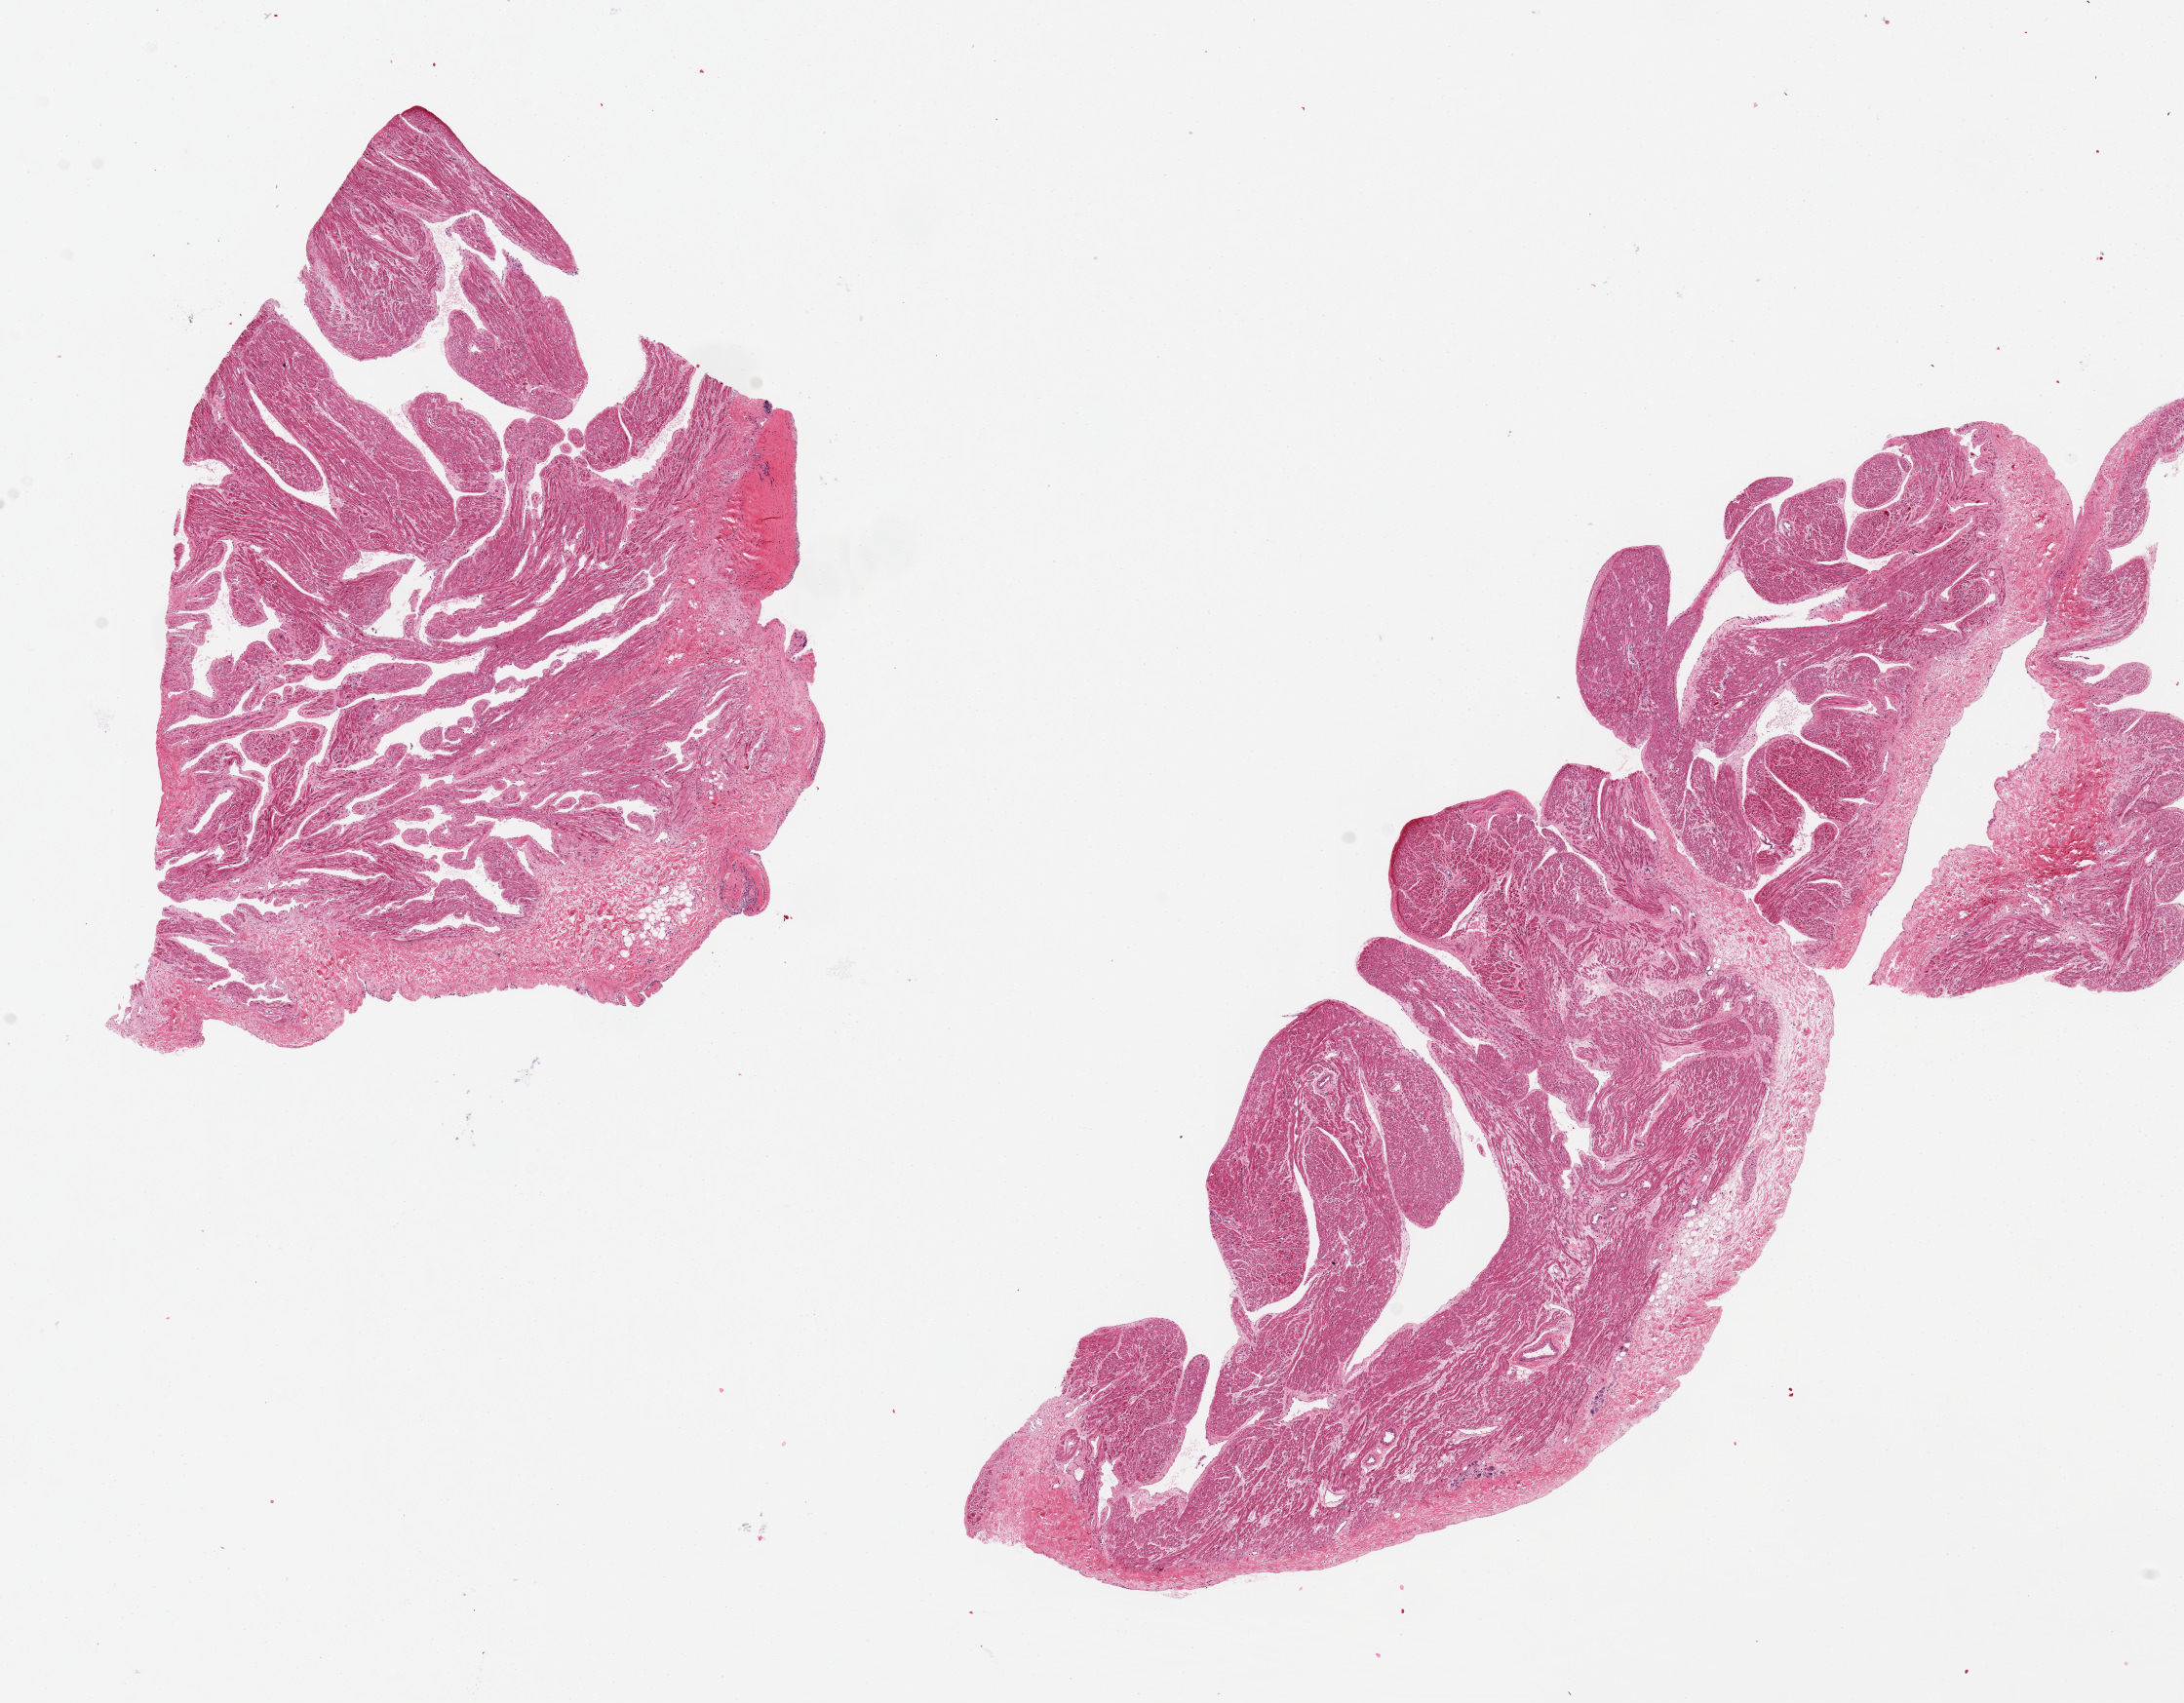
Digitized H&E-stained section, low-resolution overview of the scanned area, about 17.7 x 13.8 mm. PAXgene-fixed, paraffin-embedded tissue. Sampled site (target tissue): auricular appendage. Tissue donor sample. Donor: male.
Reviewer comment on this tissue sample: 2 pieces, 8x5 & 13x6mm; No extraneous tissue.